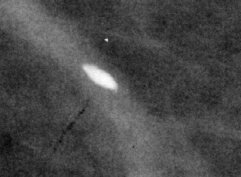
Region of interest cut from a scanned film mammogram (one marked finding); right breast; CC view; BI-RADS breast density category 1 (scale 1–4).
Marked abnormality: calcifications, morphology vascular; BI-RADS assessment category 2; benign without callback (not worked up further).